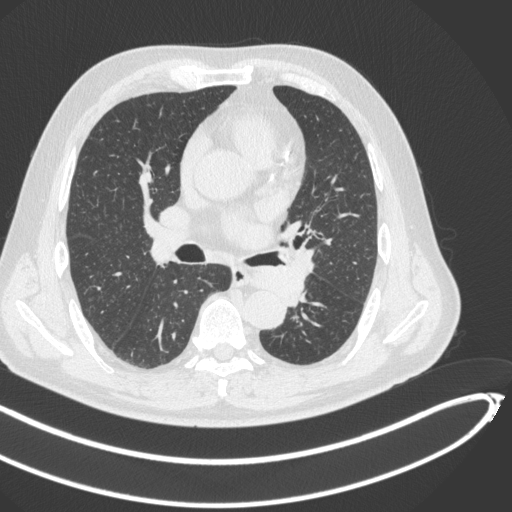
Chest CT, one axial slice; reconstruction kernel B31f; 120 kVp; lung window (W 1500 / L -600 HU); 1 mm slice thickness; 512 × 512 image matrix, field of view 400 × 400 mm. Patient: male, 64 years. From the clinical record (not read from this slice): clinical TNM (as recorded): T1c N0 M0; histopathological grade: G2.
Structures marked on this image (bounding box drawn by a radiologist):
- lung tumour (recorded histology: squamous cell carcinoma): bounding box [x1, y1, x2, y2] px = [241, 261, 306, 305]